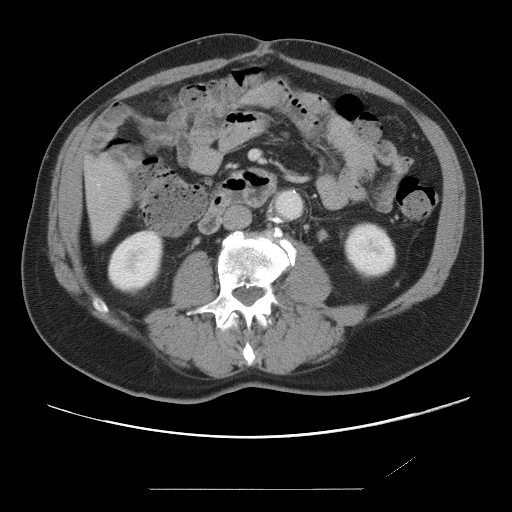
Contrast-enhanced abdominal CT, one axial slice. Position 13 of 87 along the scan axis. 120 kVp. Intravenous contrast given. Soft-tissue window (W 400 / L 40 HU). 5 mm slice thickness. 512 × 512 image matrix, field of view 406 × 406 mm. Male patient, age 74 years. Case-level facts recorded for this patient, not image findings: diagnosis: colorectal cancer liver metastases, imaged before liver resection; multiple liver metastases: yes; largest metastasis: 1.1 cm; disease in both lobes: no.
Outlined on this slice (expert manual segmentation):
- liver: bounding box <85,157,128,240> (left, top, right, bottom; pixels)
- planned liver remnant (the part of the liver to remain after resection): <85,157,128,241>